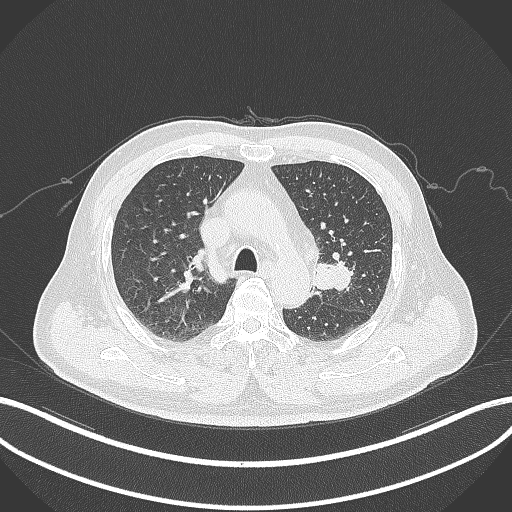
Chest CT, one axial slice. Position 208 of 286 along the scan axis. Reconstruction kernel B70f. 120 kVp. Lung window (W 1500 / L -600 HU). 1 mm slice thickness. 512 × 512 image matrix, field of view 400 × 400 mm. Male patient, age 67 years. From the clinical record (not read from this slice): clinical TNM (as recorded): T2a N1 M0; histopathological grade: G3.
Outlined on this slice (bounding box drawn by a radiologist):
- lung tumour (recorded histology: adenocarcinoma): bounding box <309,257,353,296> (left, top, right, bottom; pixels)